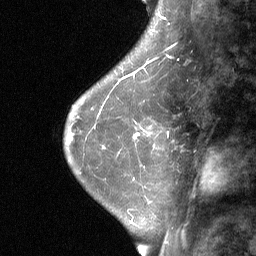
Breast MRI (dynamic contrast-enhanced), one sagittal slice; position 18 of 64 along the scan axis; dynamic contrast-enhanced study with each time point stored as its own series, time point 2 of 3 at this slice position (early post-contrast, ordered by acquisition time); 1.5 T; TE 4.8 ms, TR 27 ms; 2 mm slice thickness; 256 × 256 image matrix, field of view 180 × 180 mm. Female patient, age 42 years. From the clinical record (not read from this slice): setting: breast cancer imaged before/during neoadjuvant chemotherapy; receptor status: triple-negative.
Structures marked on this image (semi-automatically segmented with operator editing):
- analysis volume of interest (the breast-tissue region the enhancement analysis was run in; not a lesion): bounding box (x1, y1, x2, y2) in pixels: (124, 94, 179, 161)
- tumour enhancement mask (voxels above the 90 % enhancement threshold inside the analysis volume of interest): (133, 133, 139, 138)